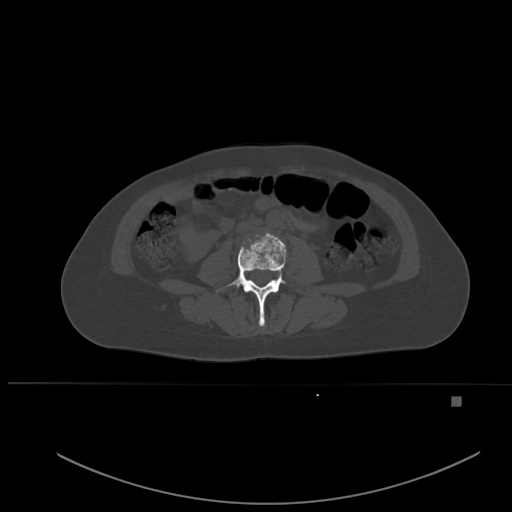
CT including the spine, one axial slice. Position 191 of 651 along the scan axis. Bone window (W 1800 / L 400 HU). 1.5 mm slice thickness. 512 × 512 image matrix, field of view 443 × 443 mm. Patient: female, 49 years. Case-level facts recorded for this patient, not image findings: primary cancer: breast; vertebrae with lytic lesions (as recorded): L3, T12, L4.
Structures marked on this image (semi-automatically segmented with operator editing):
- L3 vertebra: bounding box [x1, y1, x2, y2] px = [216, 233, 288, 327]